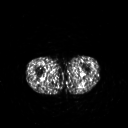
FDG PET of an extremity soft-tissue mass (from a PET/CT study), one axial slice. Position 203 of 267 along the scan axis. 3.27 mm slice thickness. 128 × 128 image matrix, field of view 500 × 500 mm. Patient: male, 54 years. Case-level facts recorded for this patient, not image findings: histological type: synovial sarcoma; site of the primary tumour: left poplietal fossa.
Annotated regions visible in this slice (expert contour drawn on MRI and transferred to this co-registered scan by the dataset authors):
- gross tumour volume (mass): bounding box [x1, y1, x2, y2] px = [78, 83, 82, 88]